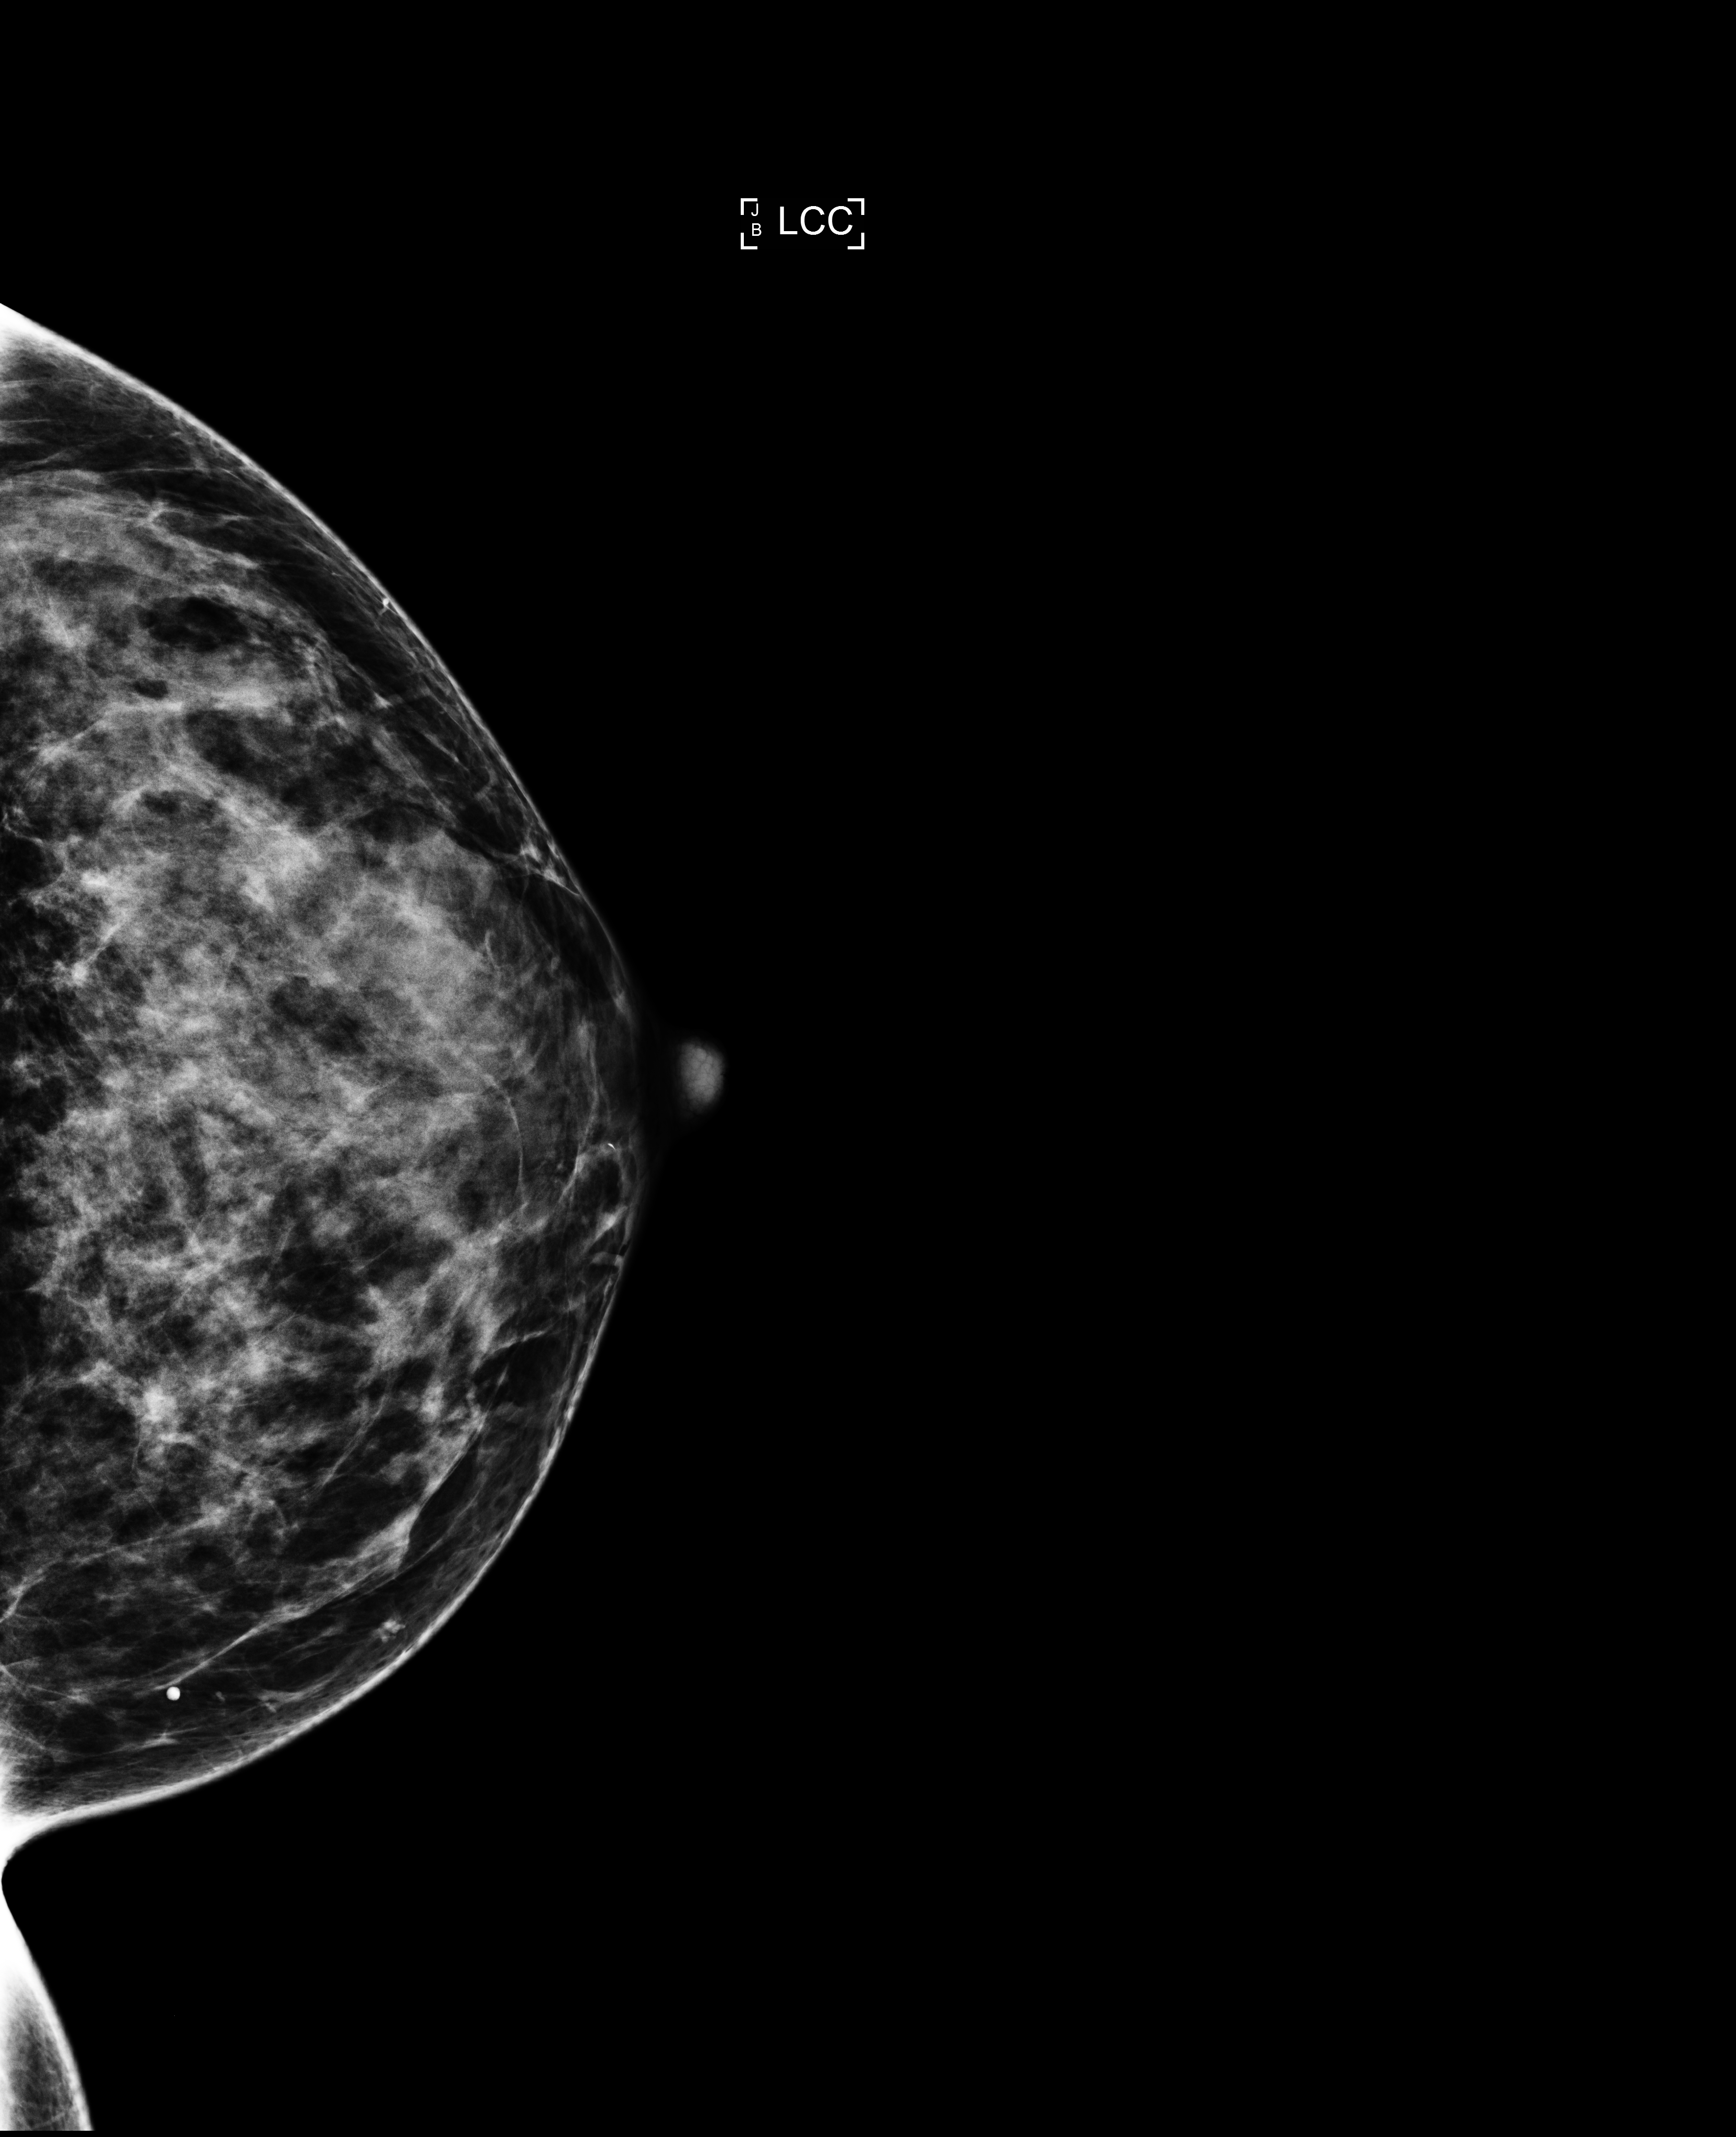
Screening examination; system: Selenia Dimensions. Patient aged 42 years (female).
Image type: full-field digital mammogram. Breast: left. Projection: craniocaudal (CC) view.